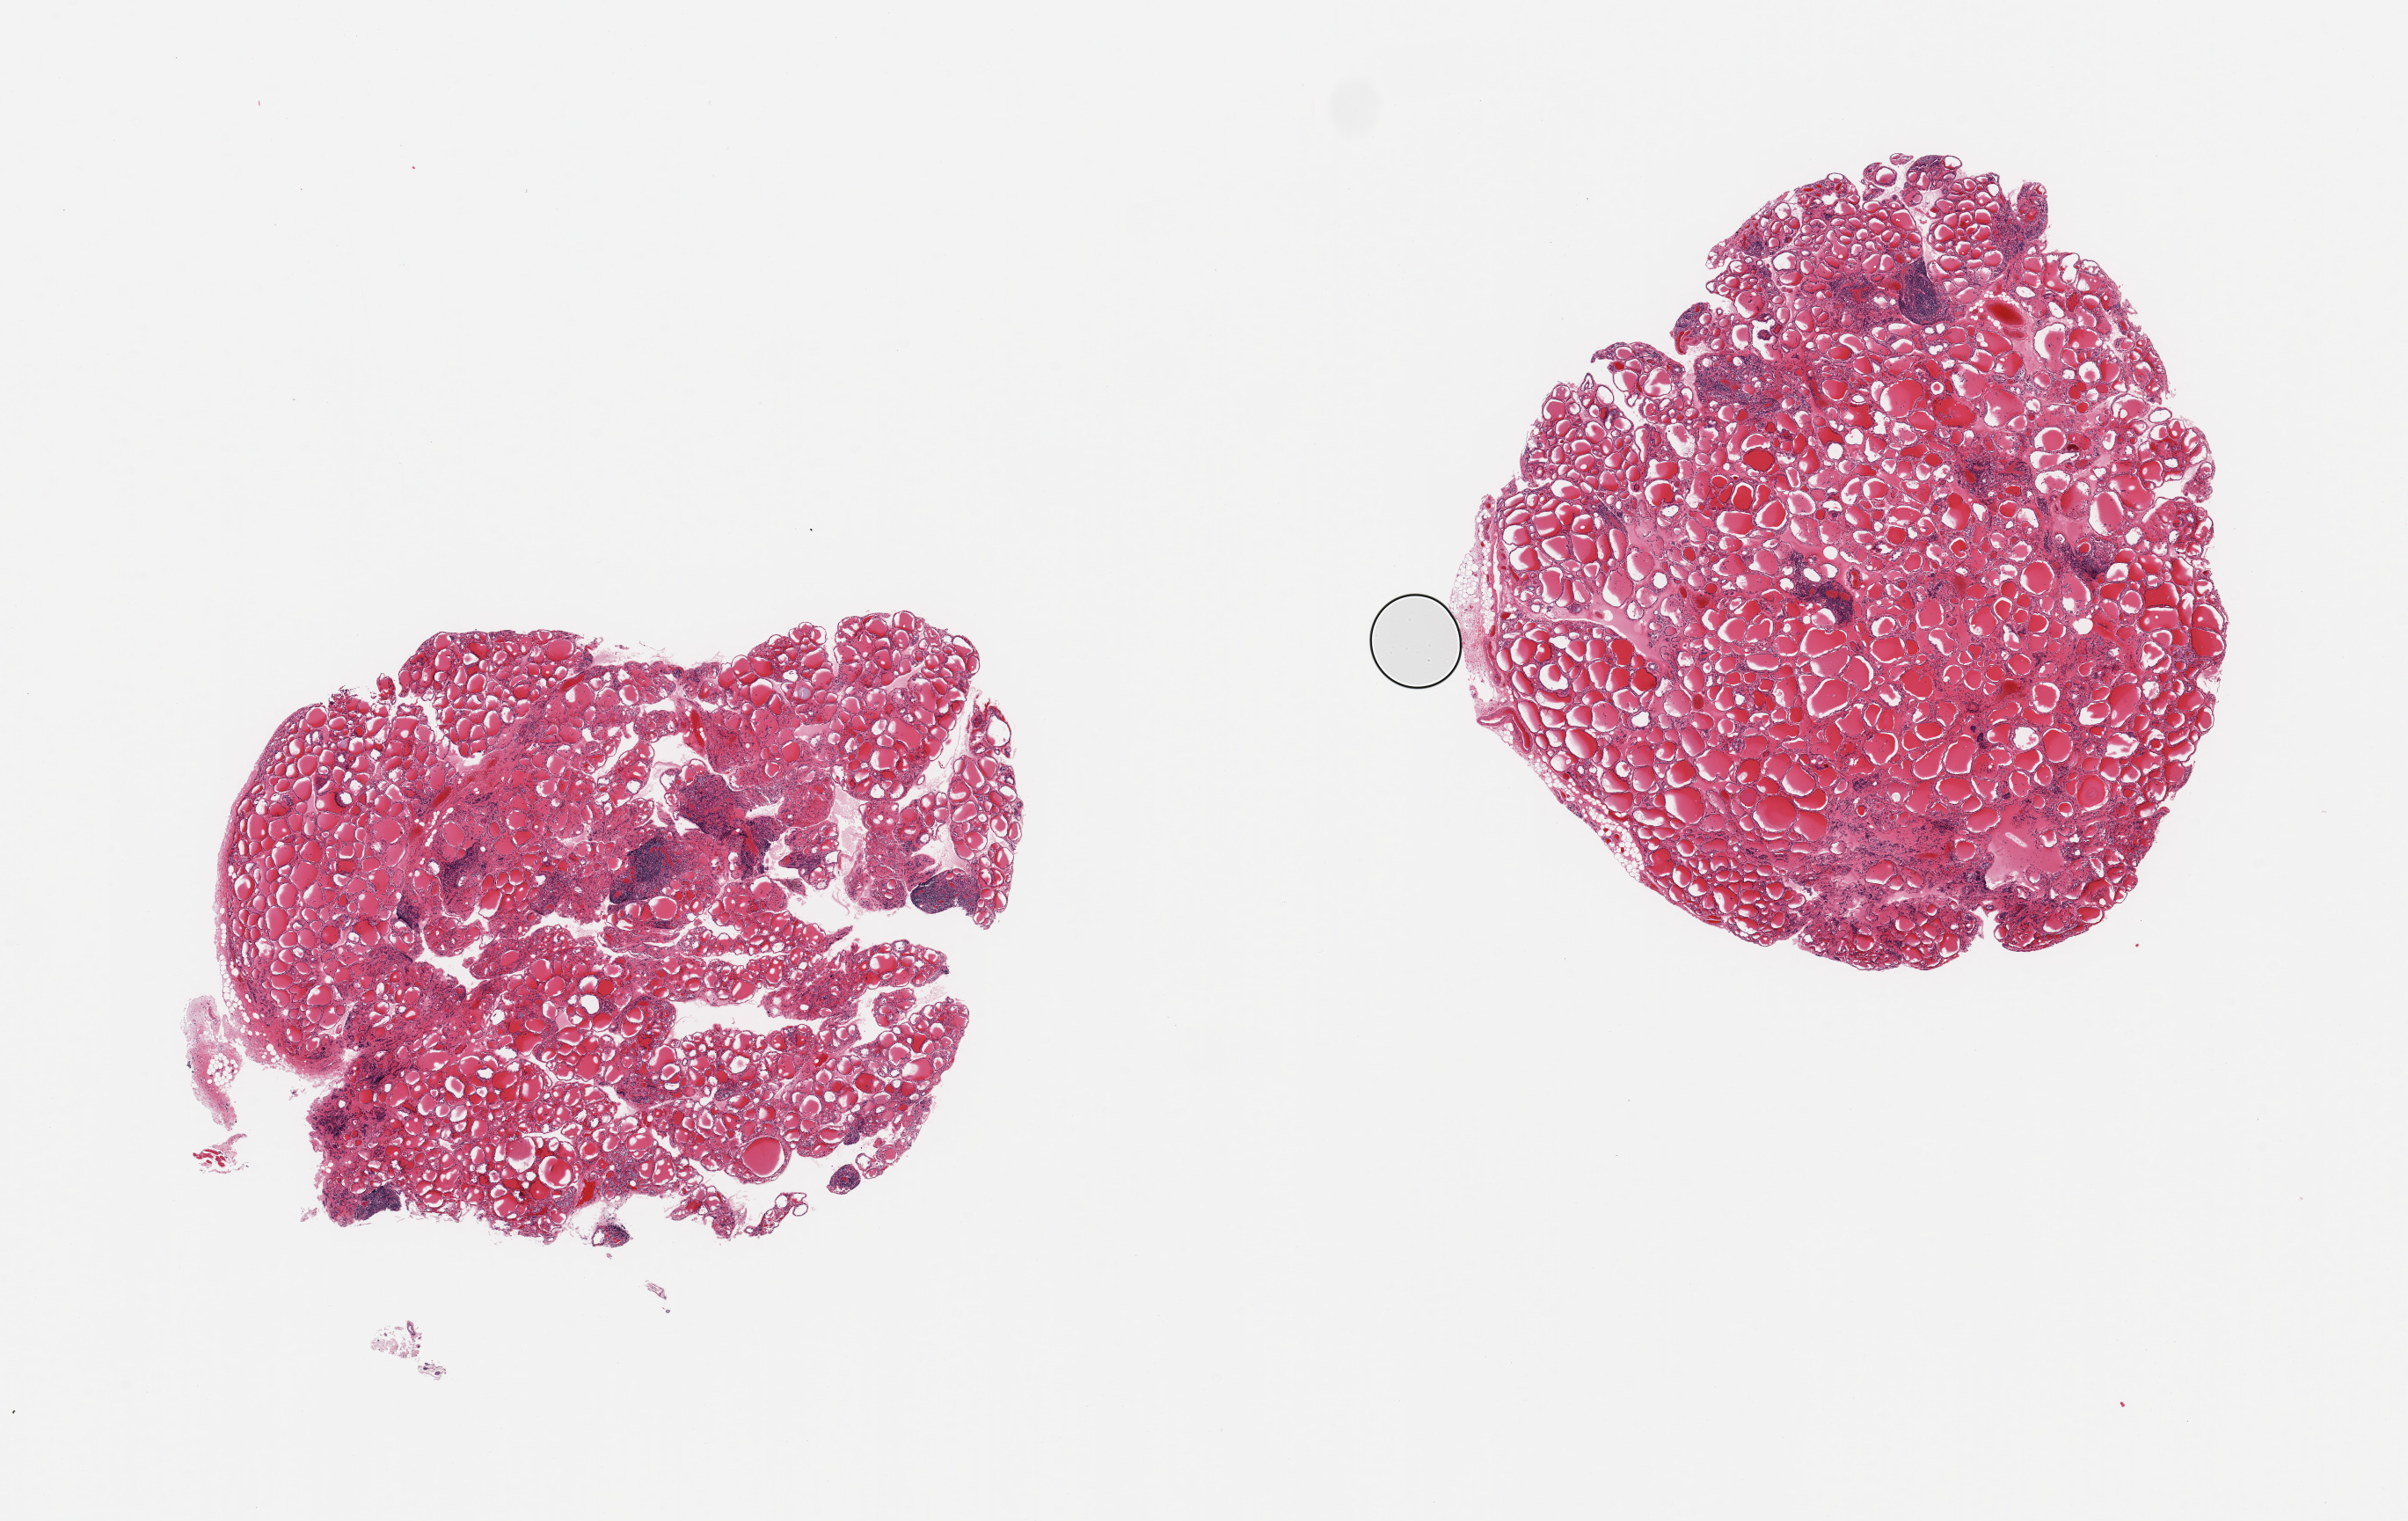
Digitized H&E-stained section, brightfield, low-resolution overview of the scanned area, about 21.7 x 13.7 mm. PAXgene-fixed, paraffin-embedded tissue. Target tissue: thyroid. Donor tissue sample. Donor sex: male.
Reviewer comment on this tissue sample: 2 pieces; scattered lymphoid collections consistent with lymphocytic thyroiditis (Hashimoto thyroiditis).